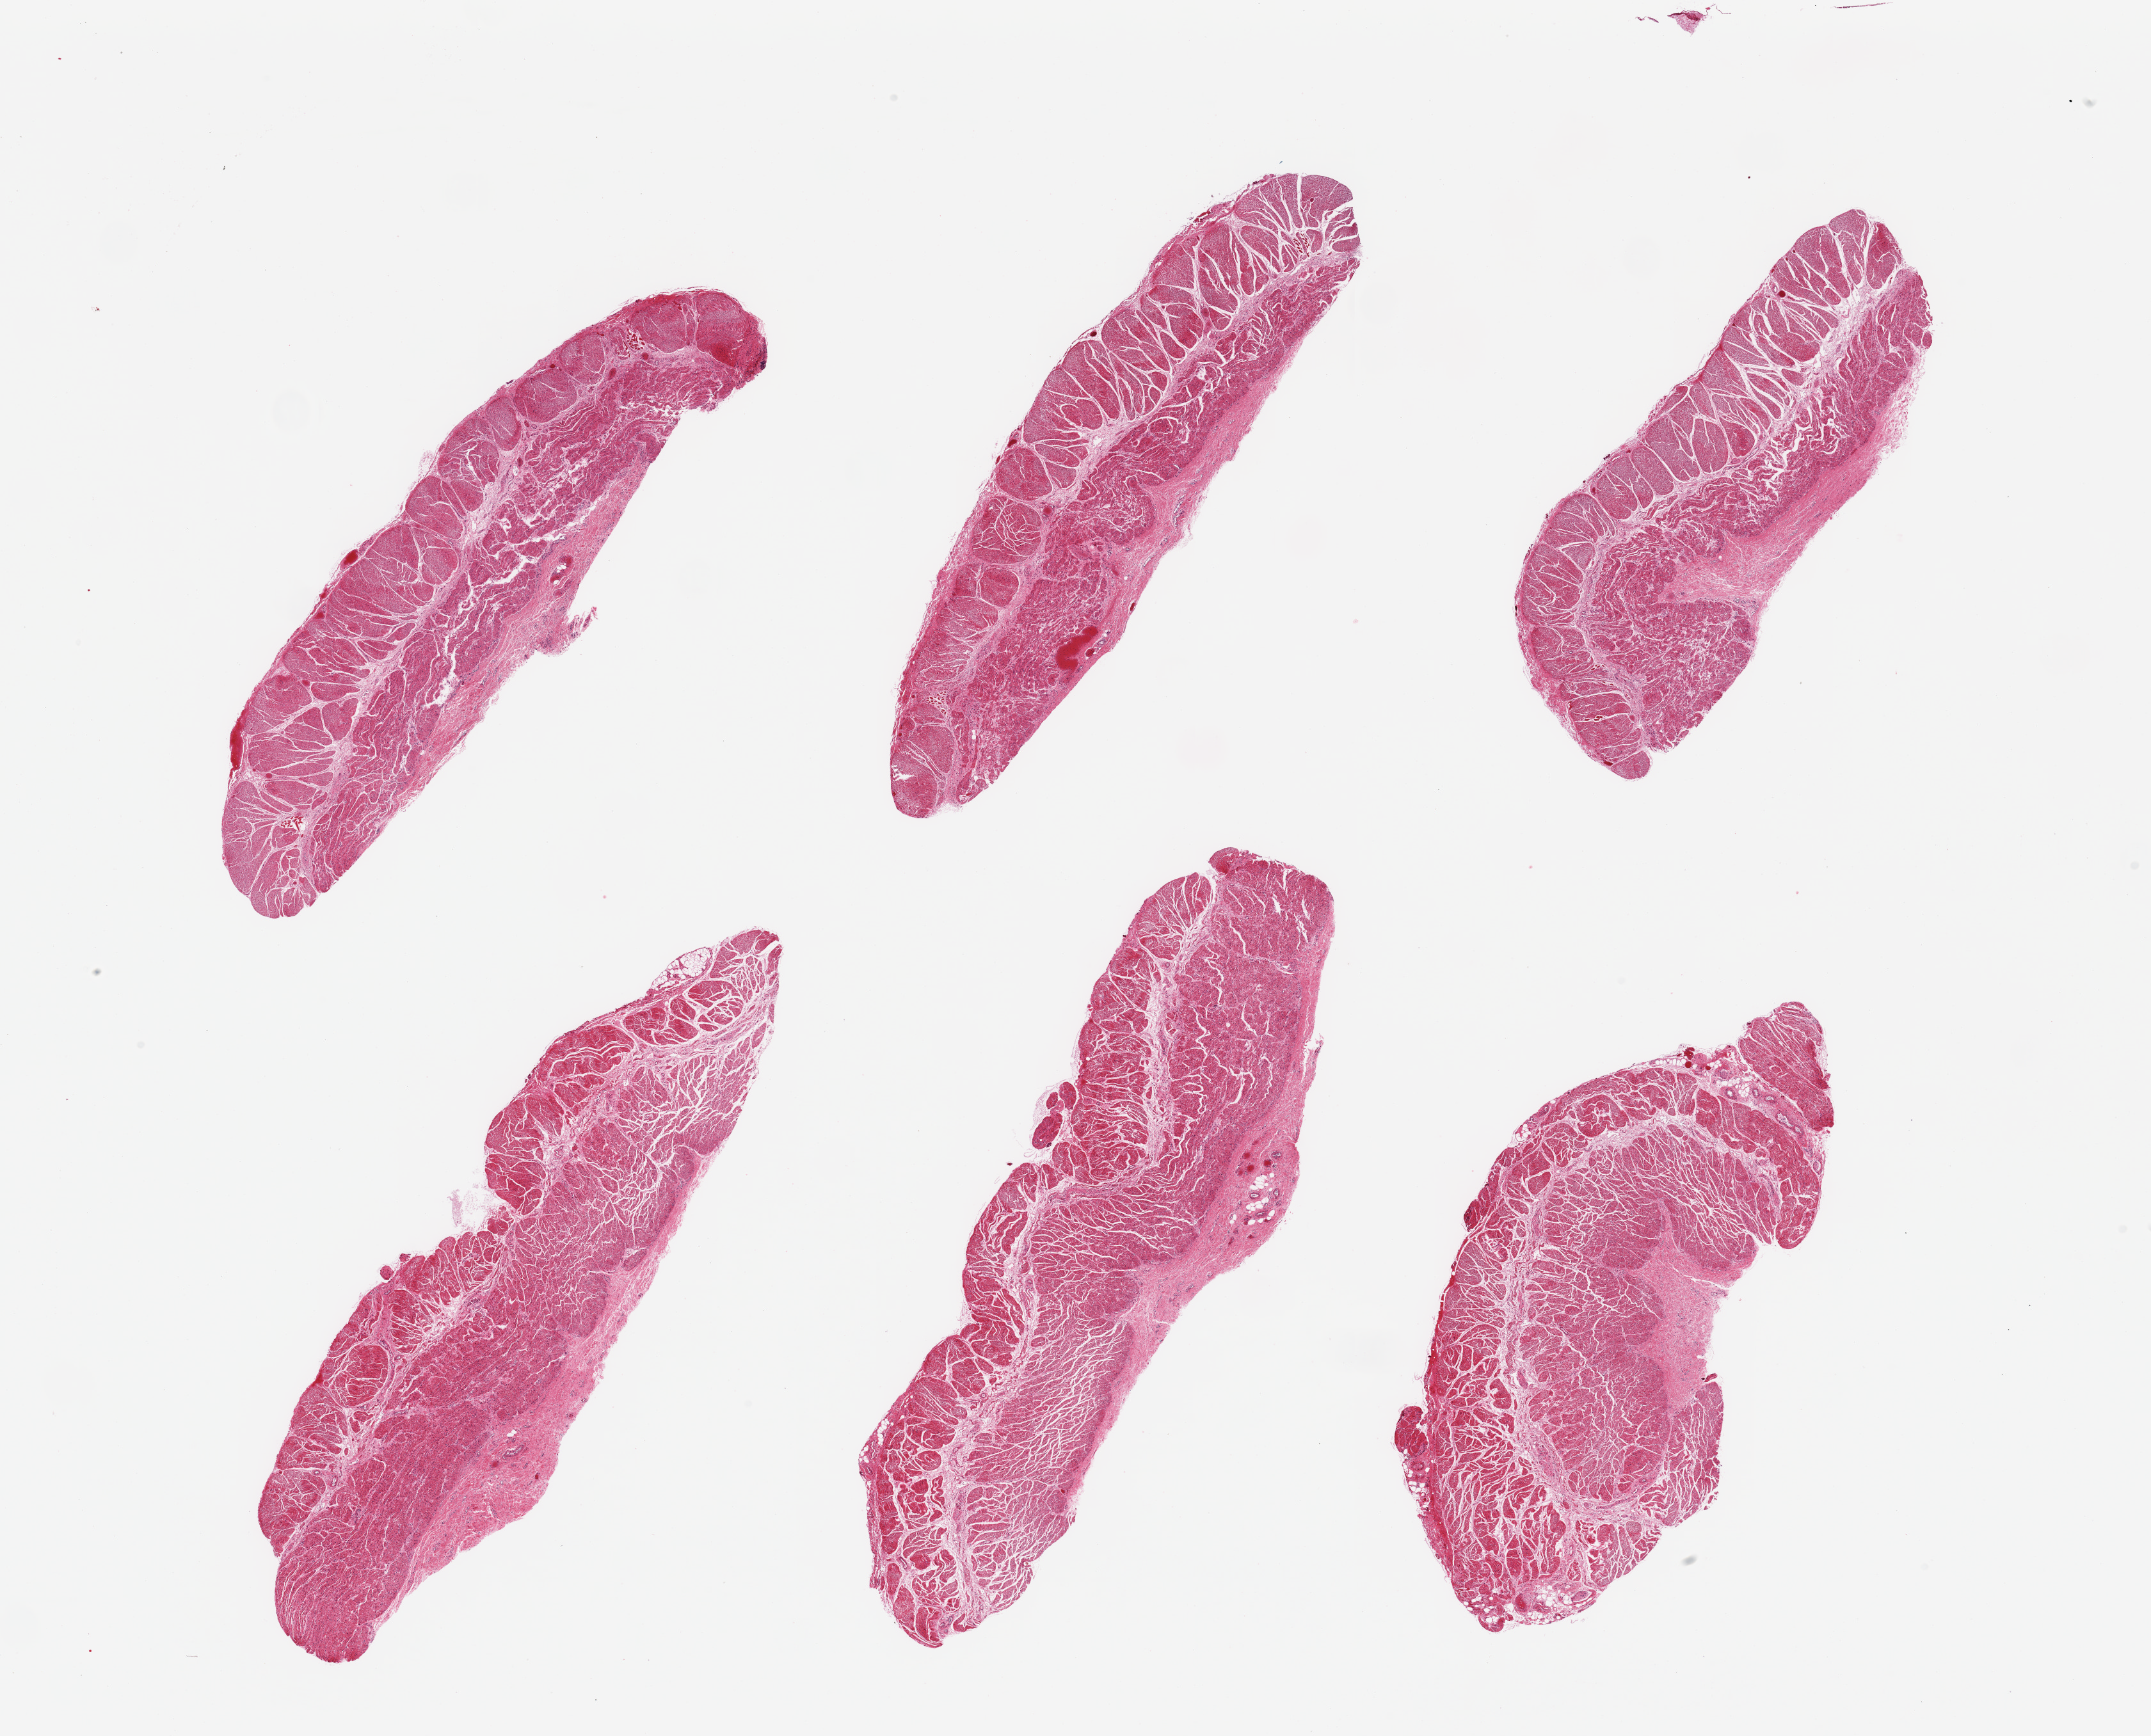
Digitized H&E-stained section, whole scanned area (about 26.6 x 21.5 mm) shown as a low-resolution overview; PAXgene-fixed, paraffin-embedded tissue; sampled site (target tissue): esophageal muscle; donor tissue sample.
Reviewer comment on this tissue sample: 6 pieces; well dissected muscularis propria; several very small foci of skeletal muscle up to 0.05mmsq in 3 pieces, <1% area.